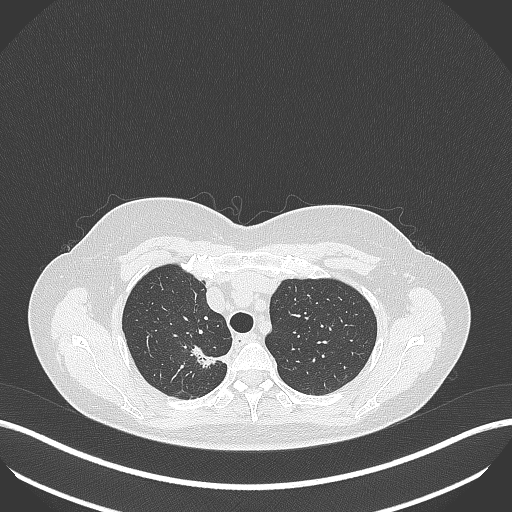
Chest CT, one axial slice. 120 kVp. Lung window (W 1500 / L -600 HU). 1 mm slice thickness. 512 × 512 image matrix. Patient: female, 65 years. From the clinical record (not read from this slice): clinical TNM (as recorded): T1b N0 M0.
Annotated regions visible in this slice (bounding box drawn by a radiologist):
- lung tumour (recorded histology: adenocarcinoma): bounding box [x1, y1, x2, y2] px = [187, 342, 230, 374]